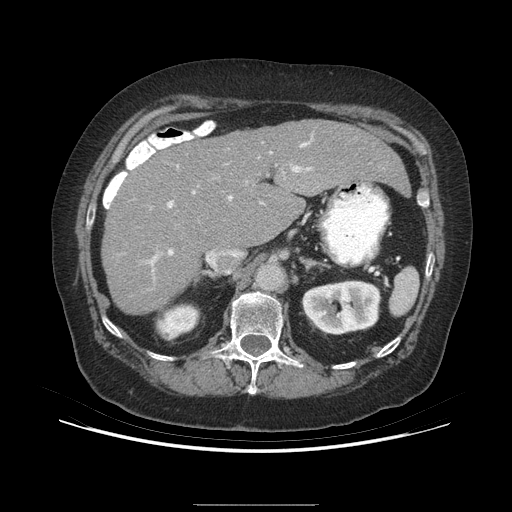
Contrast-enhanced abdominal CT (liver protocol), one axial slice; position 157 of 192 along the scan axis; soft-tissue window (W 400 / L 40 HU); 512 × 512 image matrix, field of view 400 × 400 mm. From the clinical record (not read from this slice): diagnosis: hepatocellular carcinoma (patient treated with transarterial chemoembolisation; whether this scan precedes or follows treatment is not stated here); TNM stage (as recorded): Stage-I; Child-Pugh class: A; tumour differentiation: moderately differentiated.
Structures marked on this image (semi-automatically segmented with operator editing):
- liver parenchyma outside the tumour (the mass and vessels are separate outlines, so this box may not span the whole liver): box from (x=102, y=120) to (x=406, y=314) px
- liver vessels: (x=150, y=142)–(x=311, y=266)